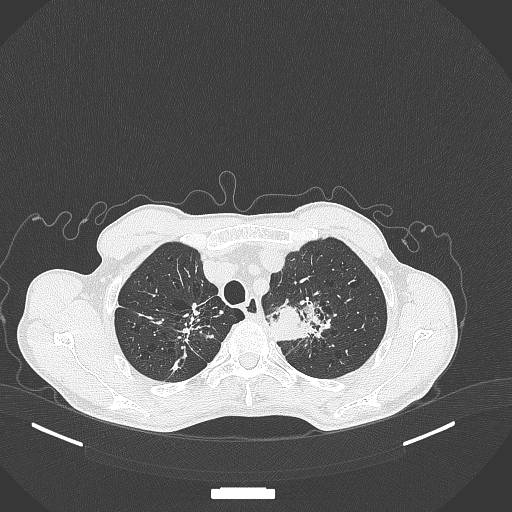
Chest CT, one axial slice; reconstruction kernel B70f; 120 kVp; lung window (W 1500 / L -600 HU); 512 × 512 image matrix. Male patient, age 65 years. Case-level facts recorded for this patient, not image findings: clinical TNM (as recorded): T2b N0 M0; histopathological grade: G2.
Outlined on this slice (rectangle marked by the reading radiologist):
- lung tumour (recorded histology: adenocarcinoma): bounding box <269,301,334,346> (left, top, right, bottom; pixels)